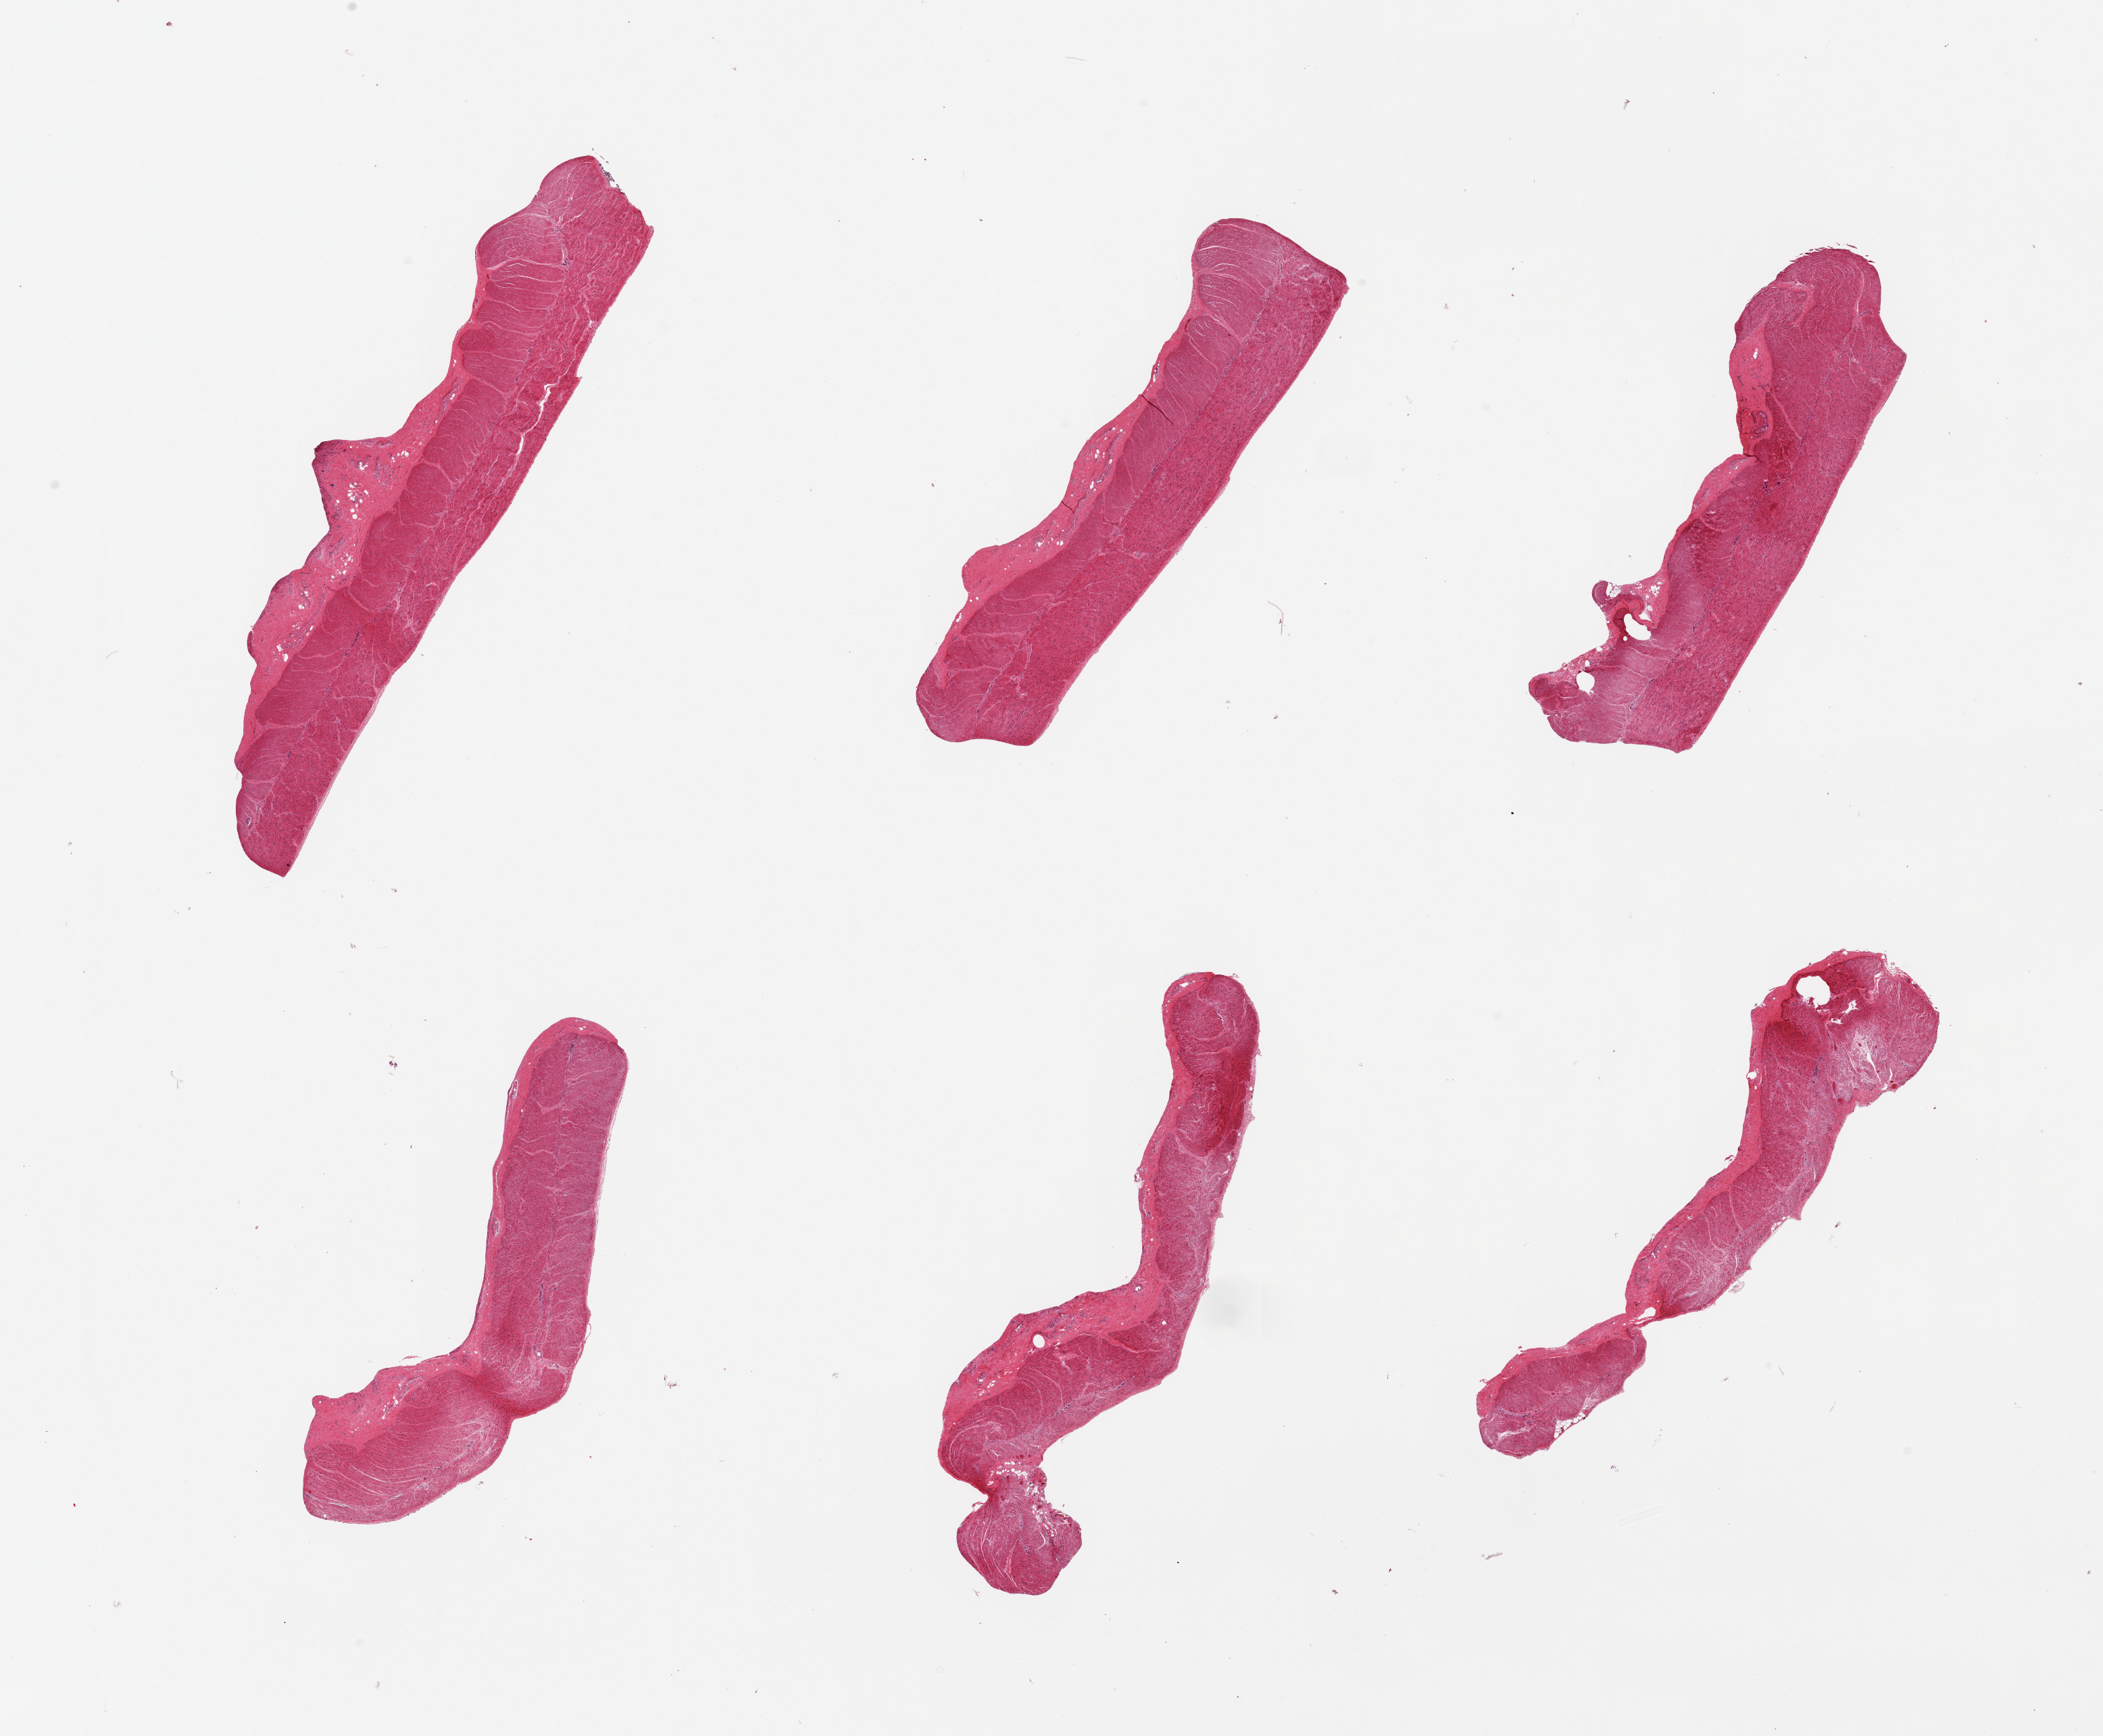
Haematoxylin and eosin whole-slide image, brightfield, whole scanned area (about 24.6 x 20.3 mm, acquisition: 20x scan) shown as a low-resolution overview; PAXgene-fixed paraffin-embedded (PFPE) section; sampled site (target tissue): sigmoid colon; donor tissue sample. Donor: female.
Pathologist's review note for this sample: 6 pieces, congested, unusually autolyzed.